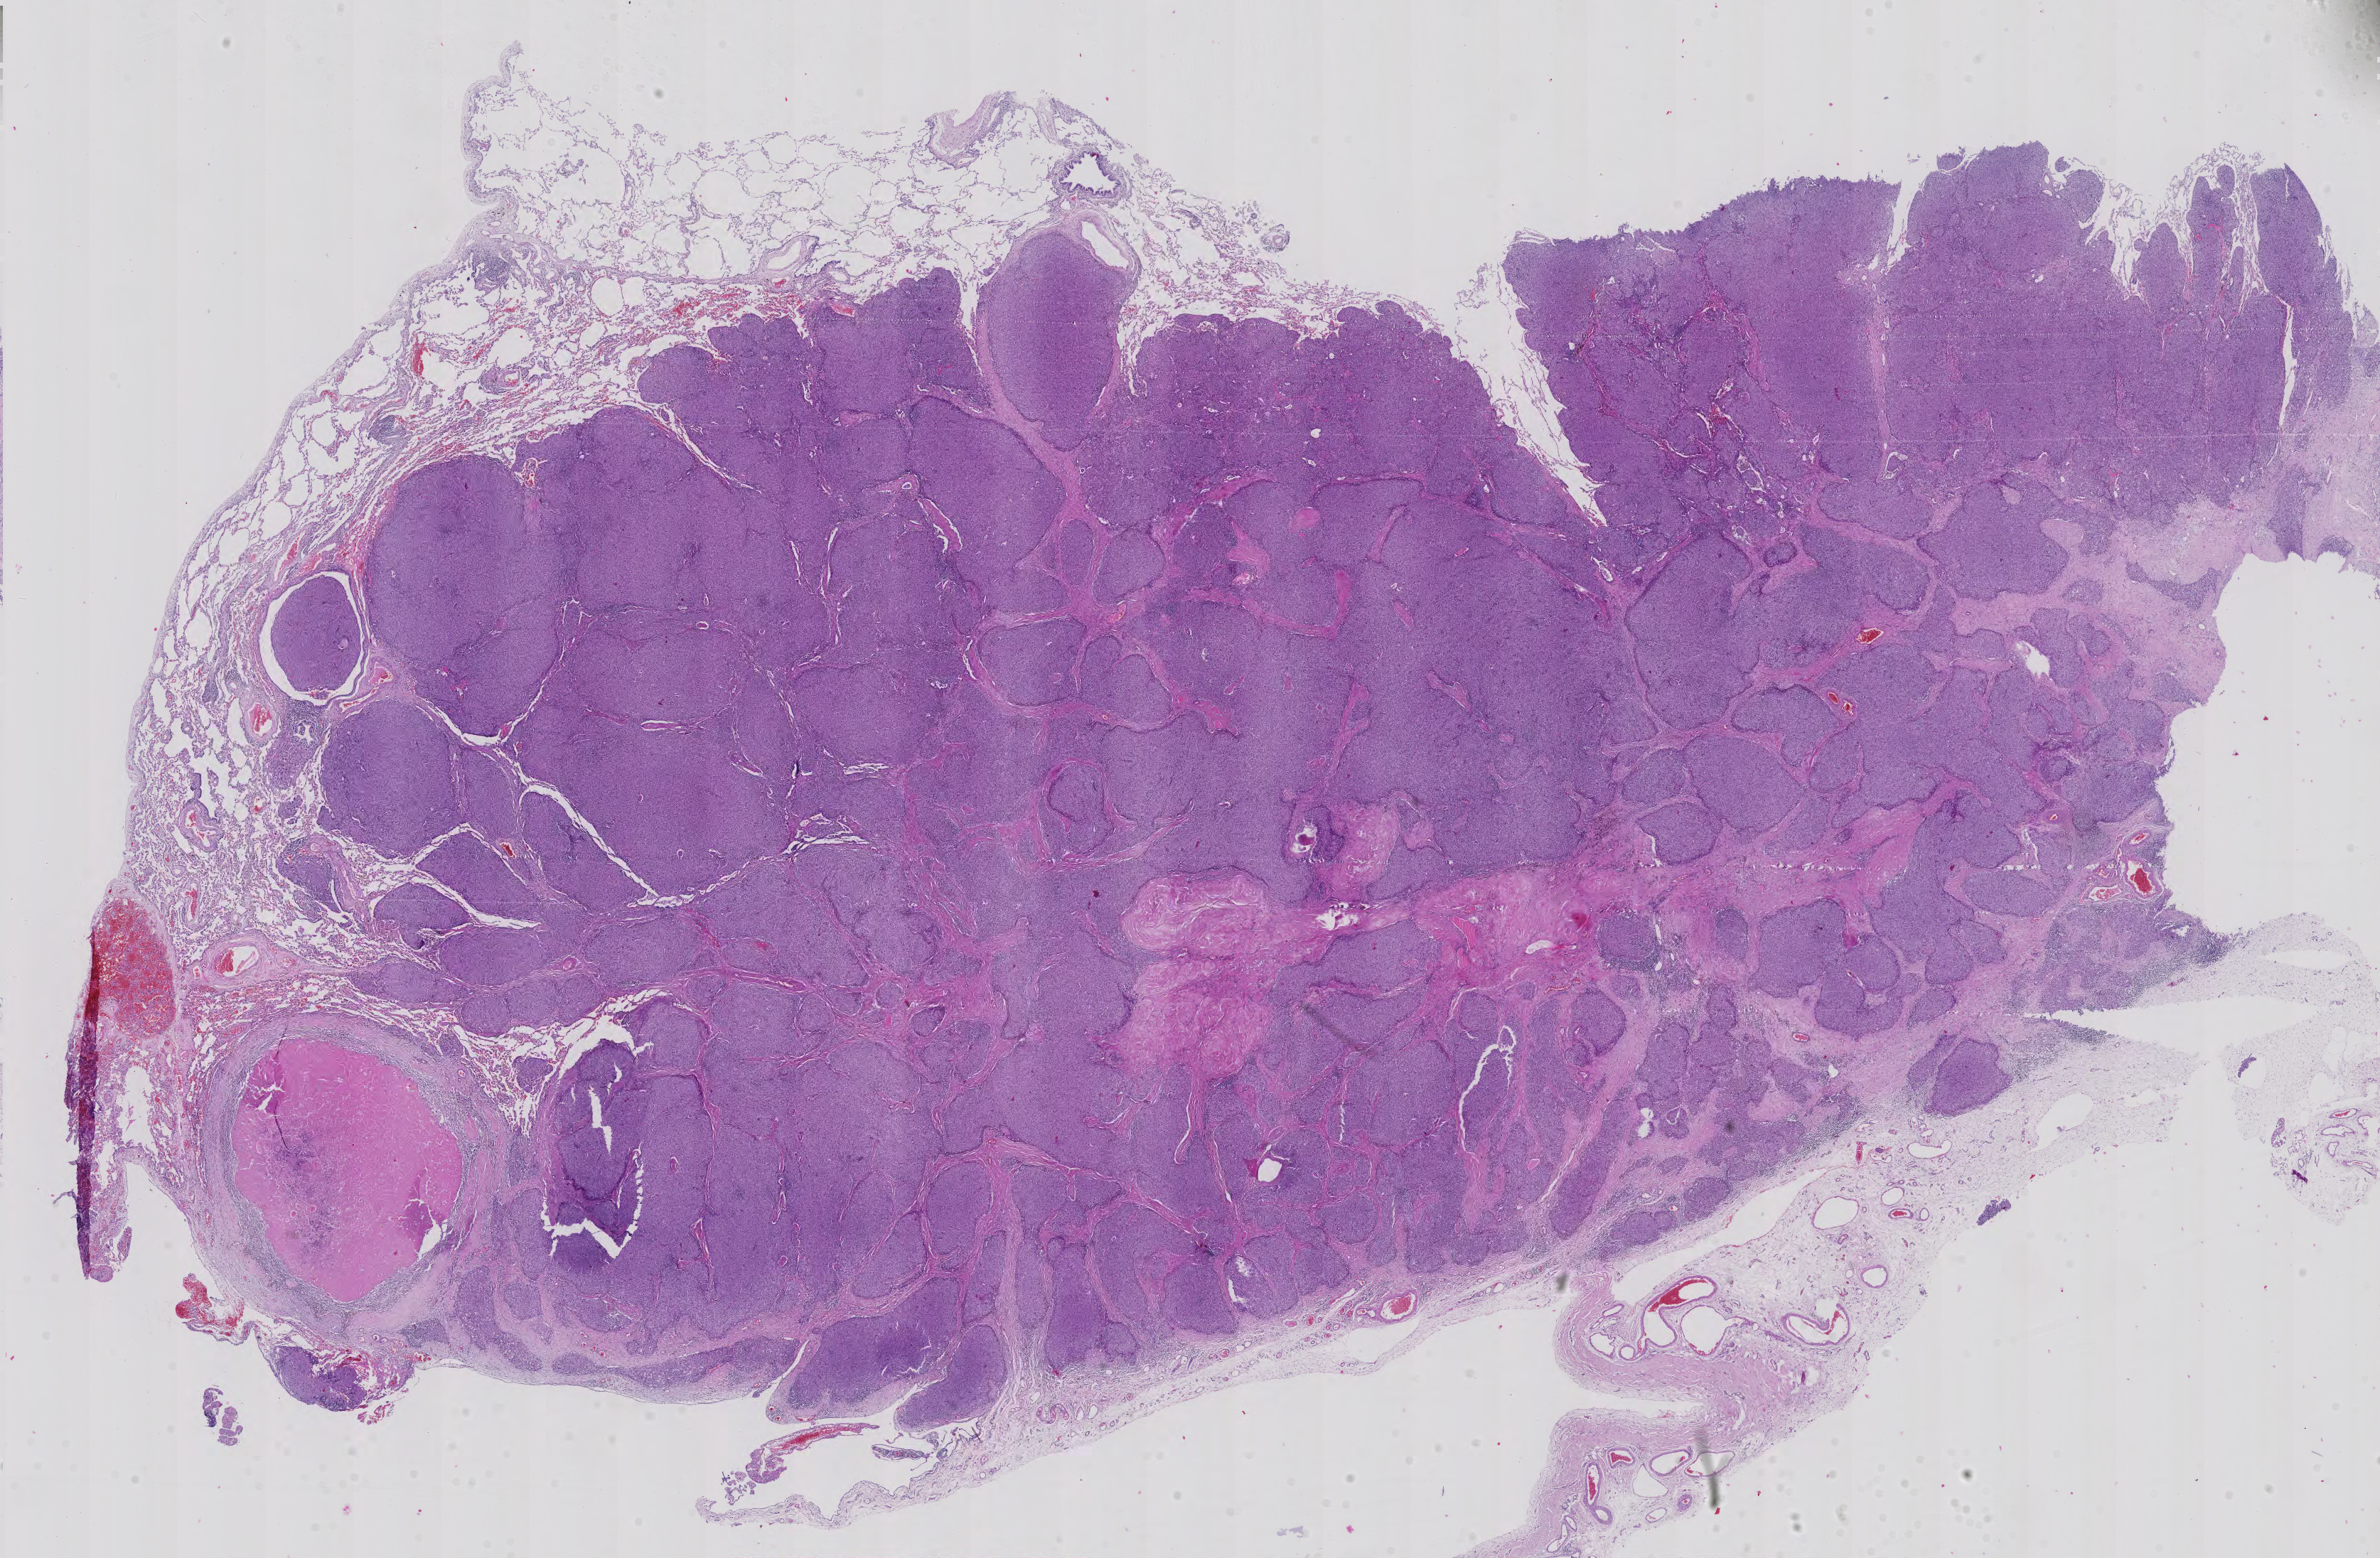
Digitized Hematoxylin and eosin (H&E) stained tissue section (whole slide) — low-resolution overview of the scanned area, about 24.4 x 16.0 mm (acquisition: 40x scan); formalin-fixed paraffin-embedded (FFPE) diagnostic section; primary tumour sample from the thymus. Female patient; age at initial diagnosis 71 years.
Histologic diagnosis: Thymoma, type AB, malignant (anterior mediastinum).